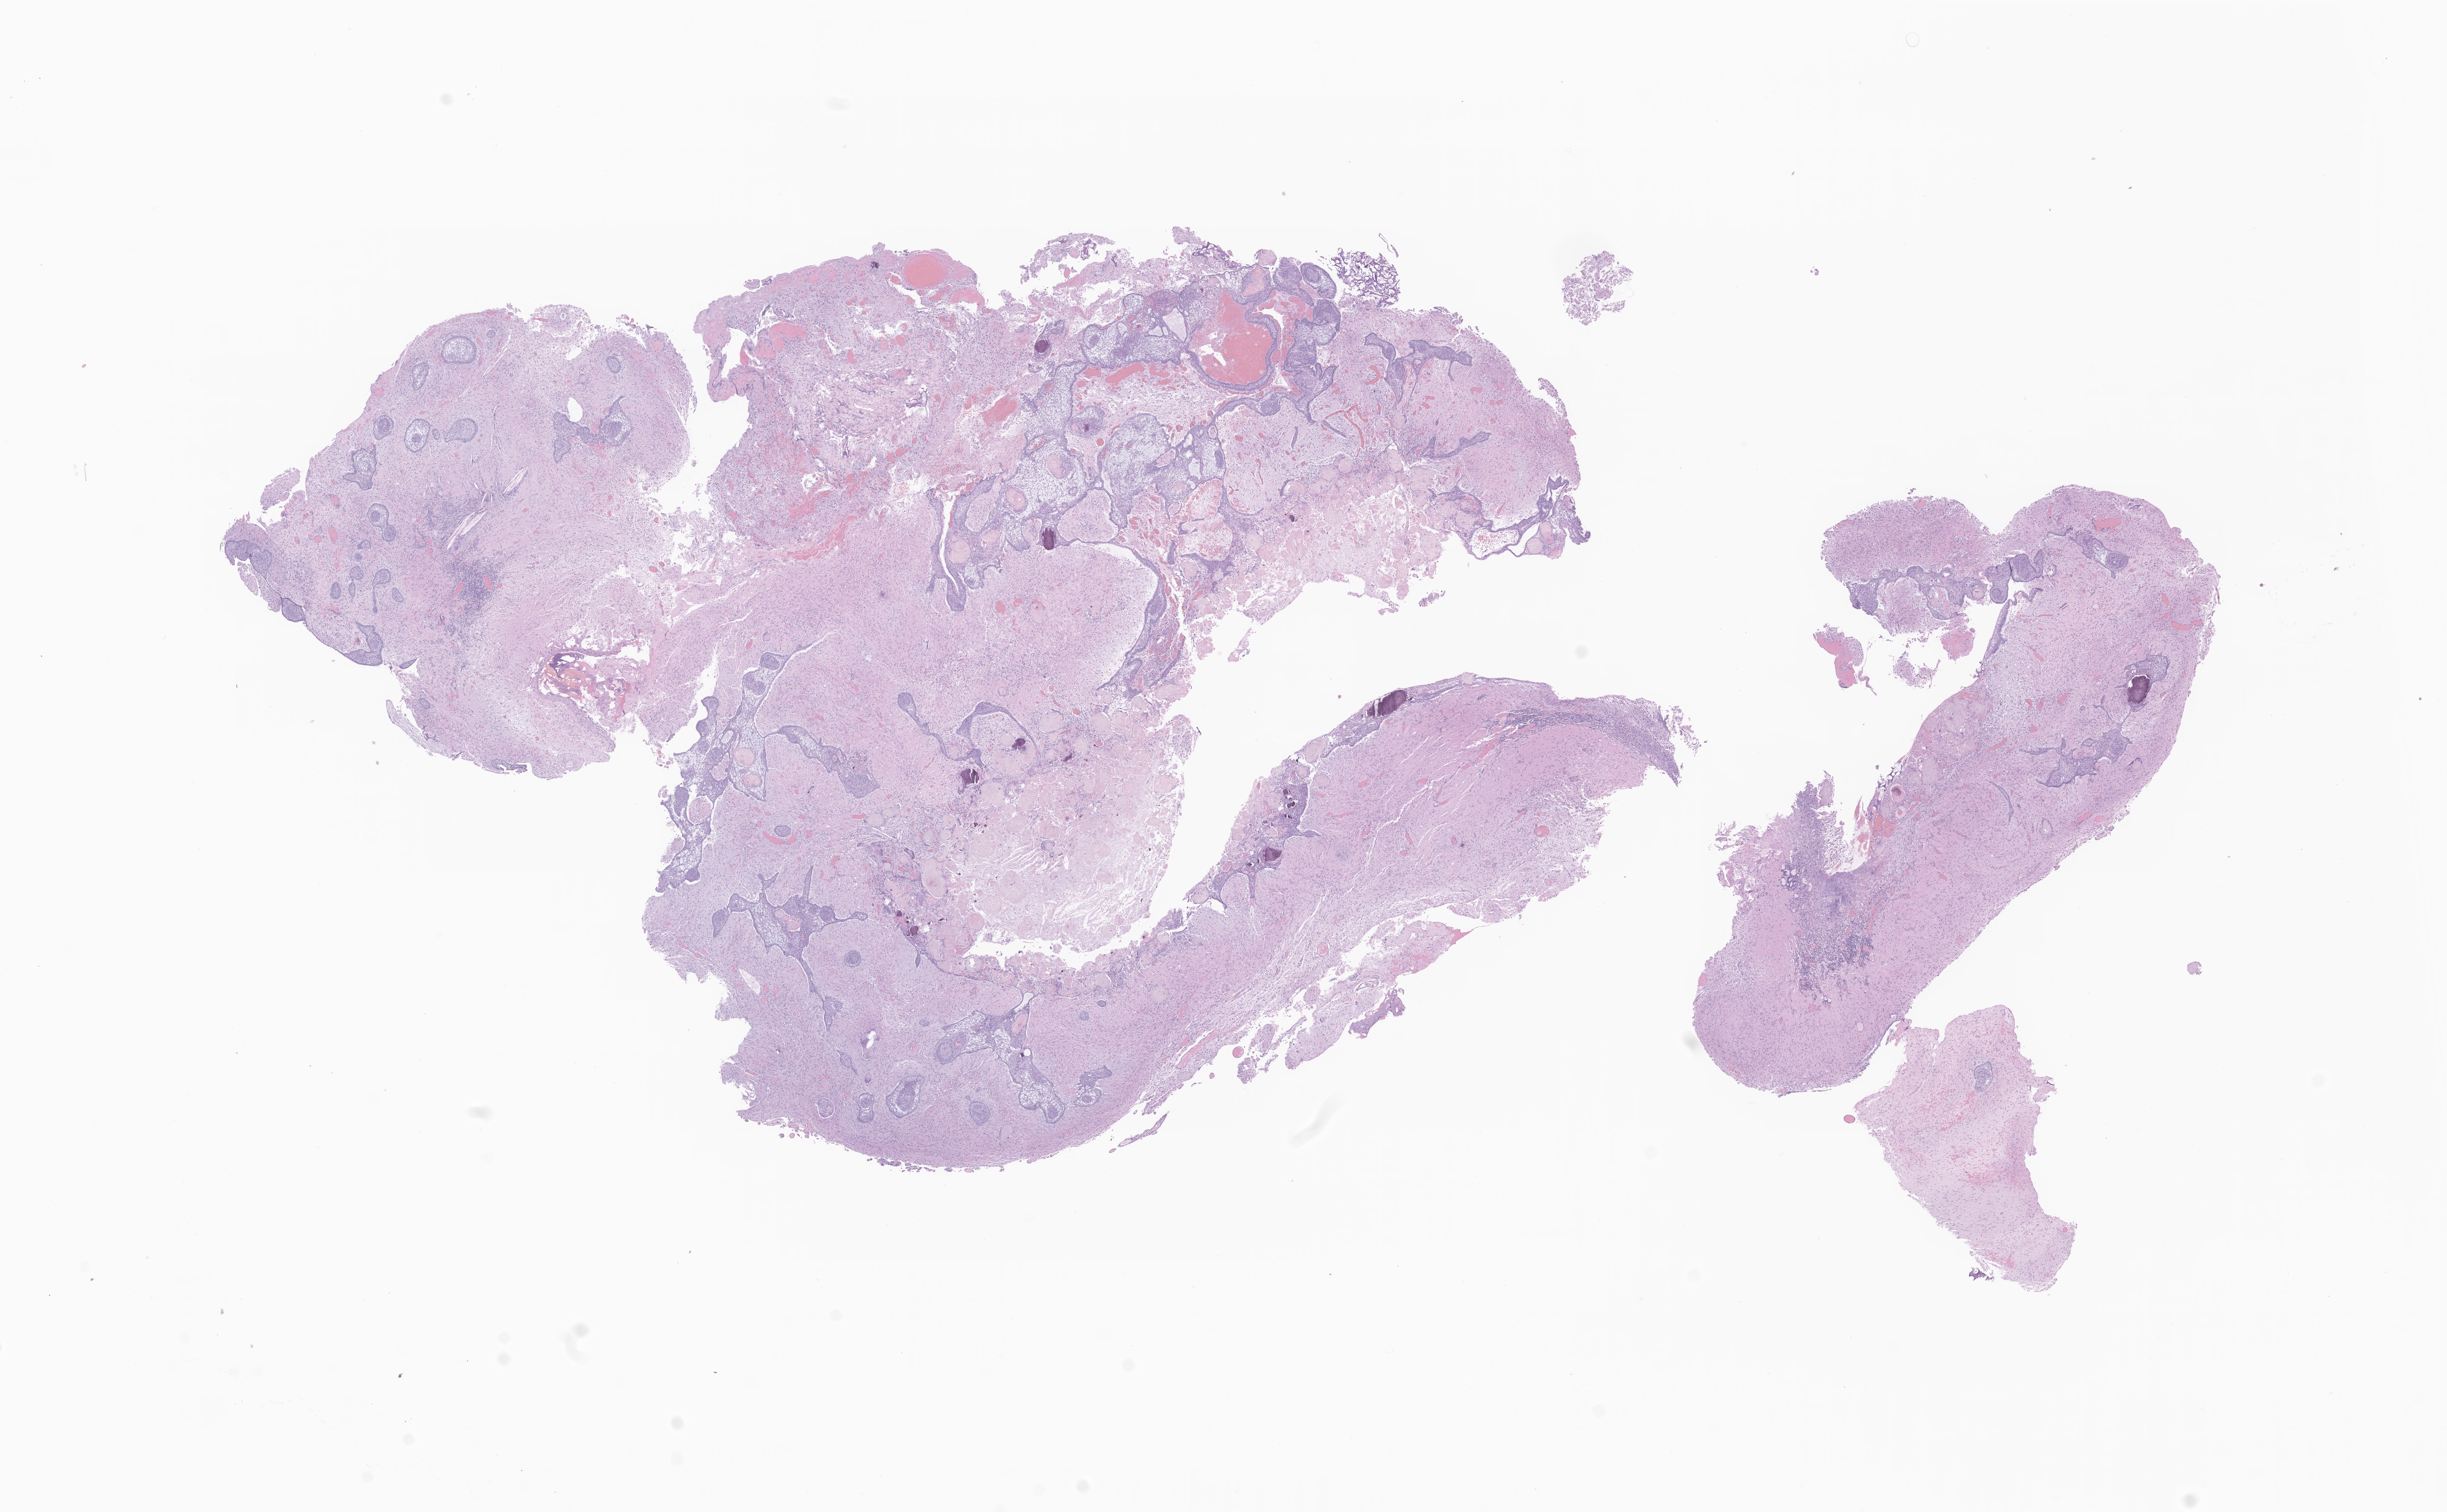
Haematoxylin and eosin whole-slide image of tumor tissue from the cerebral ventricle, shown as a low-resolution overview of the whole scanned area (about 20.2 x 12.5 mm); FFPE section. Patient: female, age 104 months (8 years 8 months).
Recorded diagnosis: Craniopharyngioma, NOS.